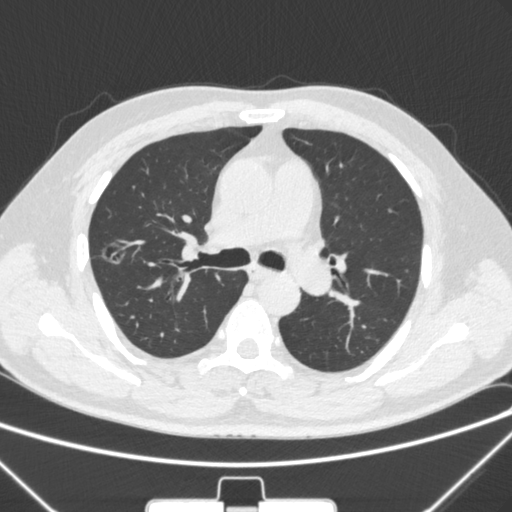
Chest CT, one axial slice; slice 195 of 320 in the series (ordered by position); 120 kVp; lung window (W 1500 / L -600 HU); 1 mm slice thickness; 512 × 512 image matrix, field of view 350 × 350 mm. Patient: male, 58 years. Case-level facts recorded for this patient, not image findings: clinical TNM (as recorded): T1c N0 M0.
Structures marked on this image (rectangle marked by the reading radiologist):
- lung tumour (recorded histology: adenocarcinoma): bounding box <92,229,131,274> (left, top, right, bottom; pixels)